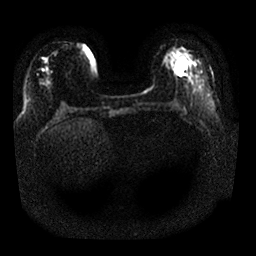
Breast MRI, one axial slice; slice 7 of 25 in the series (ordered by position); diffusion-weighted series; image 2 of 4 stored at this slice position (different b-values; order by instance number); 1.5 T; 4 mm slice thickness; 256 × 256 image matrix. Female patient.
Outlined on this slice (manually delineated by an expert):
- tumour on diffusion-weighted imaging: bounding box <169,52,187,74> (left, top, right, bottom; pixels)